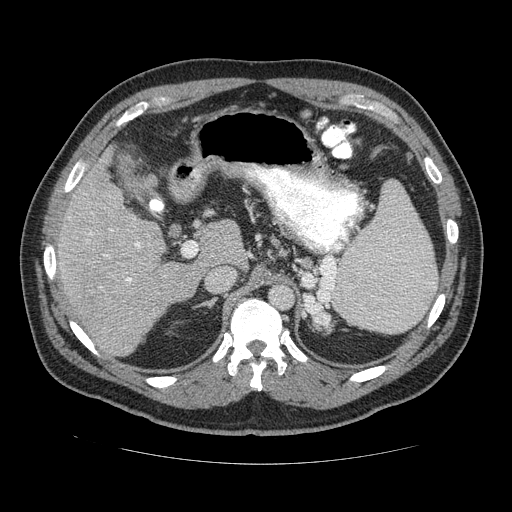
Contrast-enhanced abdominal CT (liver protocol), one axial slice. Slice 81 of 113 in the series (ordered by position). Soft-tissue window (W 400 / L 40 HU). 2.5 mm slice thickness. 512 × 512 image matrix. From the clinical record (not read from this slice): diagnosis: hepatocellular carcinoma (patient treated with transarterial chemoembolisation; whether this scan precedes or follows treatment is not stated here); TNM stage (as recorded): Stage-II; Child-Pugh class: B; tumour differentiation: moderately differentiated.
Annotated regions visible in this slice (semi-automatic segmentation, software-assisted and operator-edited):
- liver parenchyma outside the tumour (the mass and vessels are separate outlines, so this box may not span the whole liver): box from (x=50, y=140) to (x=240, y=356) px
- liver vessels: (x=51, y=236)–(x=146, y=283)